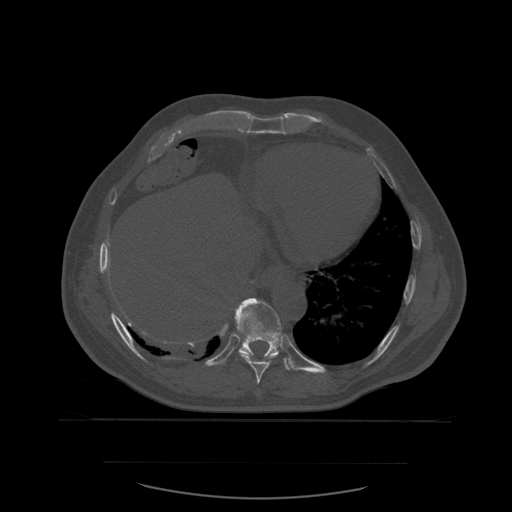
CT including the spine, one axial slice. Position 331 of 590 along the scan axis. Bone window (W 1800 / L 400 HU). 1.25 mm slice thickness. 512 × 512 image matrix. Patient age 71 years. Case-level facts recorded for this patient, not image findings: primary cancer: lung.
Structures marked on this image (semi-automatically segmented with operator editing):
- T10 vertebra: bounding box (x1, y1, x2, y2) in pixels: (235, 298, 291, 371)
- T9 vertebra: (239, 352, 278, 385)